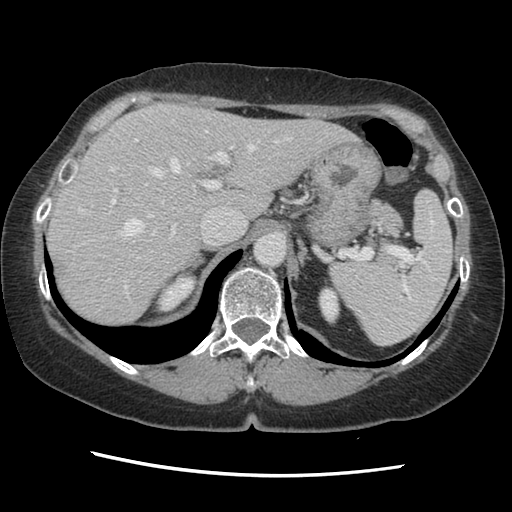
Contrast-enhanced abdominal CT, one axial slice; position 98 of 141 along the scan axis; 120 kVp; soft-tissue window (W 400 / L 40 HU); 2.5 mm slice thickness; 512 × 512 image matrix, field of view 330 × 330 mm. Female patient, age 61 years. From the clinical record (not read from this slice): diagnosis: colorectal cancer liver metastases, imaged before liver resection; multiple liver metastases: no; largest metastasis: 2.4 cm; disease in both lobes: no.
Outlined on this slice (outlined manually by an expert reader):
- hepatic veins: bounding box (x1, y1, x2, y2) in pixels: (78, 120, 291, 296)
- liver: (47, 105, 351, 327)
- planned liver remnant (the part of the liver to remain after resection): (47, 105, 351, 327)
- portal vein (with intrahepatic branches): (111, 138, 233, 241)